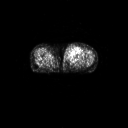
FDG PET of an extremity soft-tissue mass (from a PET/CT study), one axial slice; slice 44 of 91 in the series (ordered by position); 128 × 128 image matrix, field of view 700 × 700 mm. Patient: female, 74 years. Case-level facts recorded for this patient, not image findings: histological type: pleomorphic leiomyosarcoma; grade: high; site of the primary tumour: left thigh.
Annotated regions visible in this slice (expert contour drawn on MRI and transferred to this co-registered scan by the dataset authors):
- gross tumour volume including surrounding oedema: box from (x=65, y=47) to (x=80, y=61) px
- gross tumour volume (mass): (x=70, y=47)–(x=77, y=55)